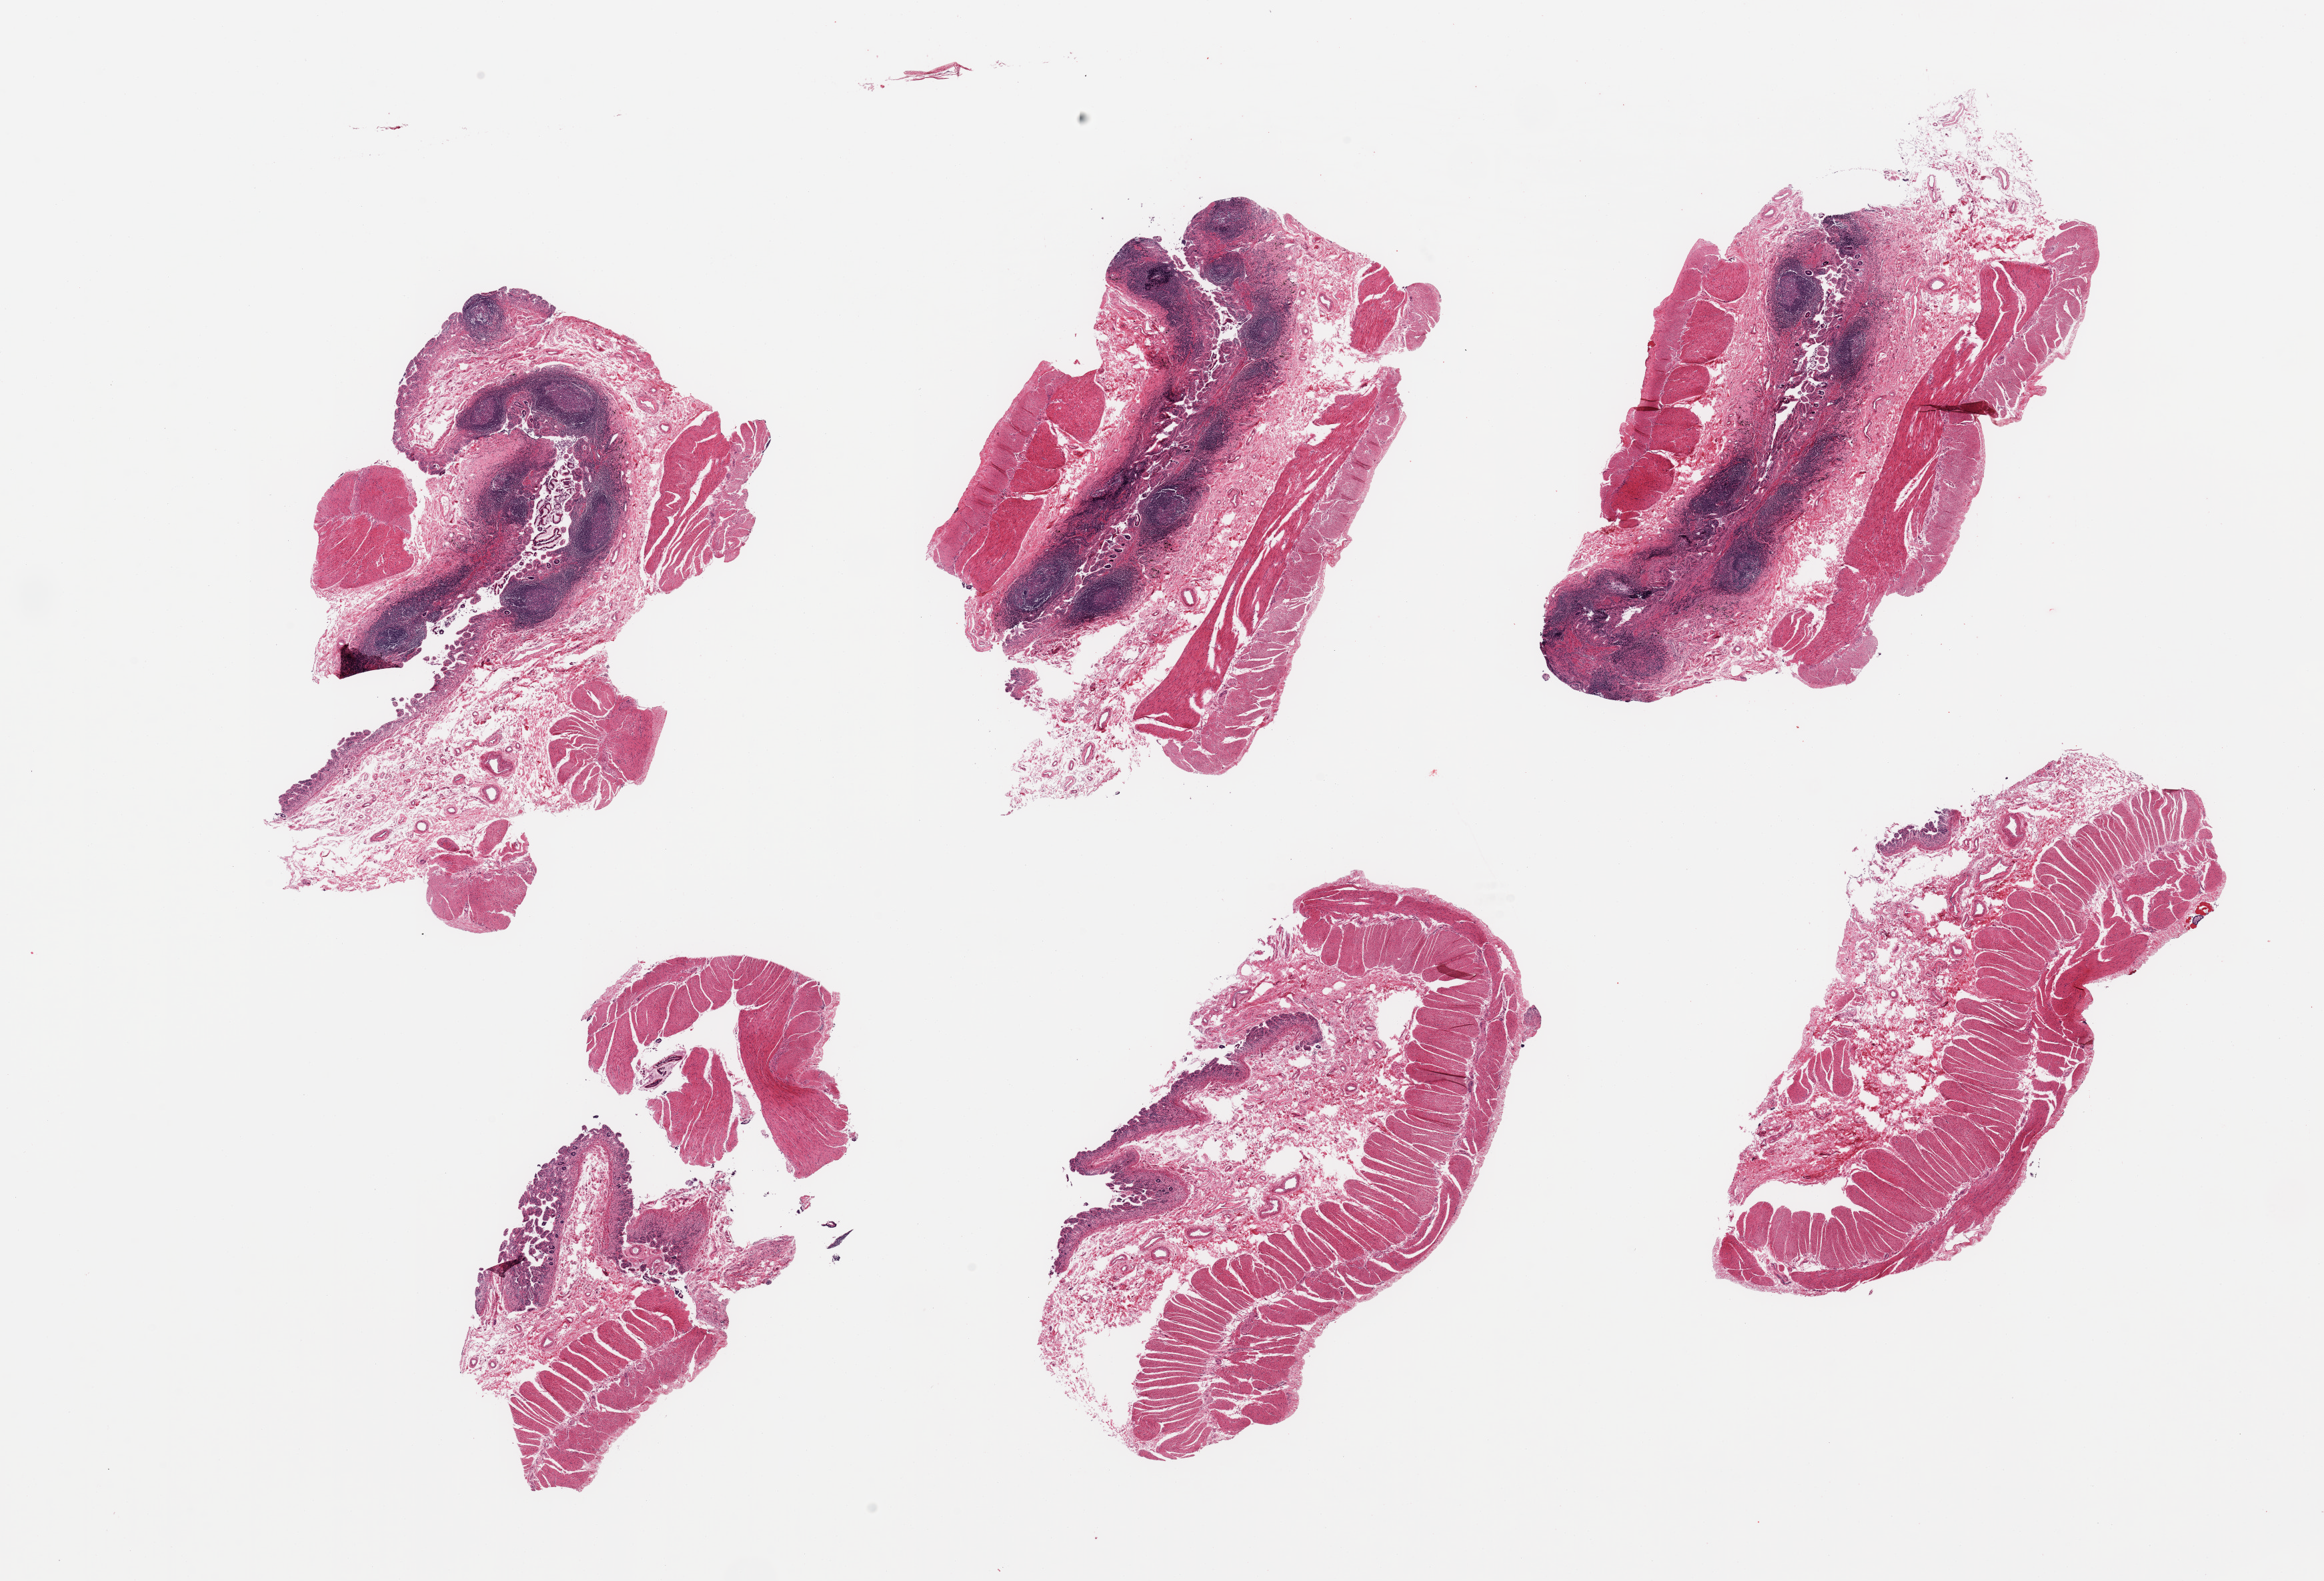
Whole-slide image, hematoxylin and eosin (H&E) stain — a low-resolution overview of the entire scanned area, about 27.6 x 18.8 mm (acquisition: 20x scan); PAXgene-fixed, paraffin-embedded tissue; section of ileum (target tissue); tissue donor sample.
Pathologist's review note for this sample: 6 pieces; variable representation of autolyzed mucosa, excellent lymphoid component, and abundant muscularis.